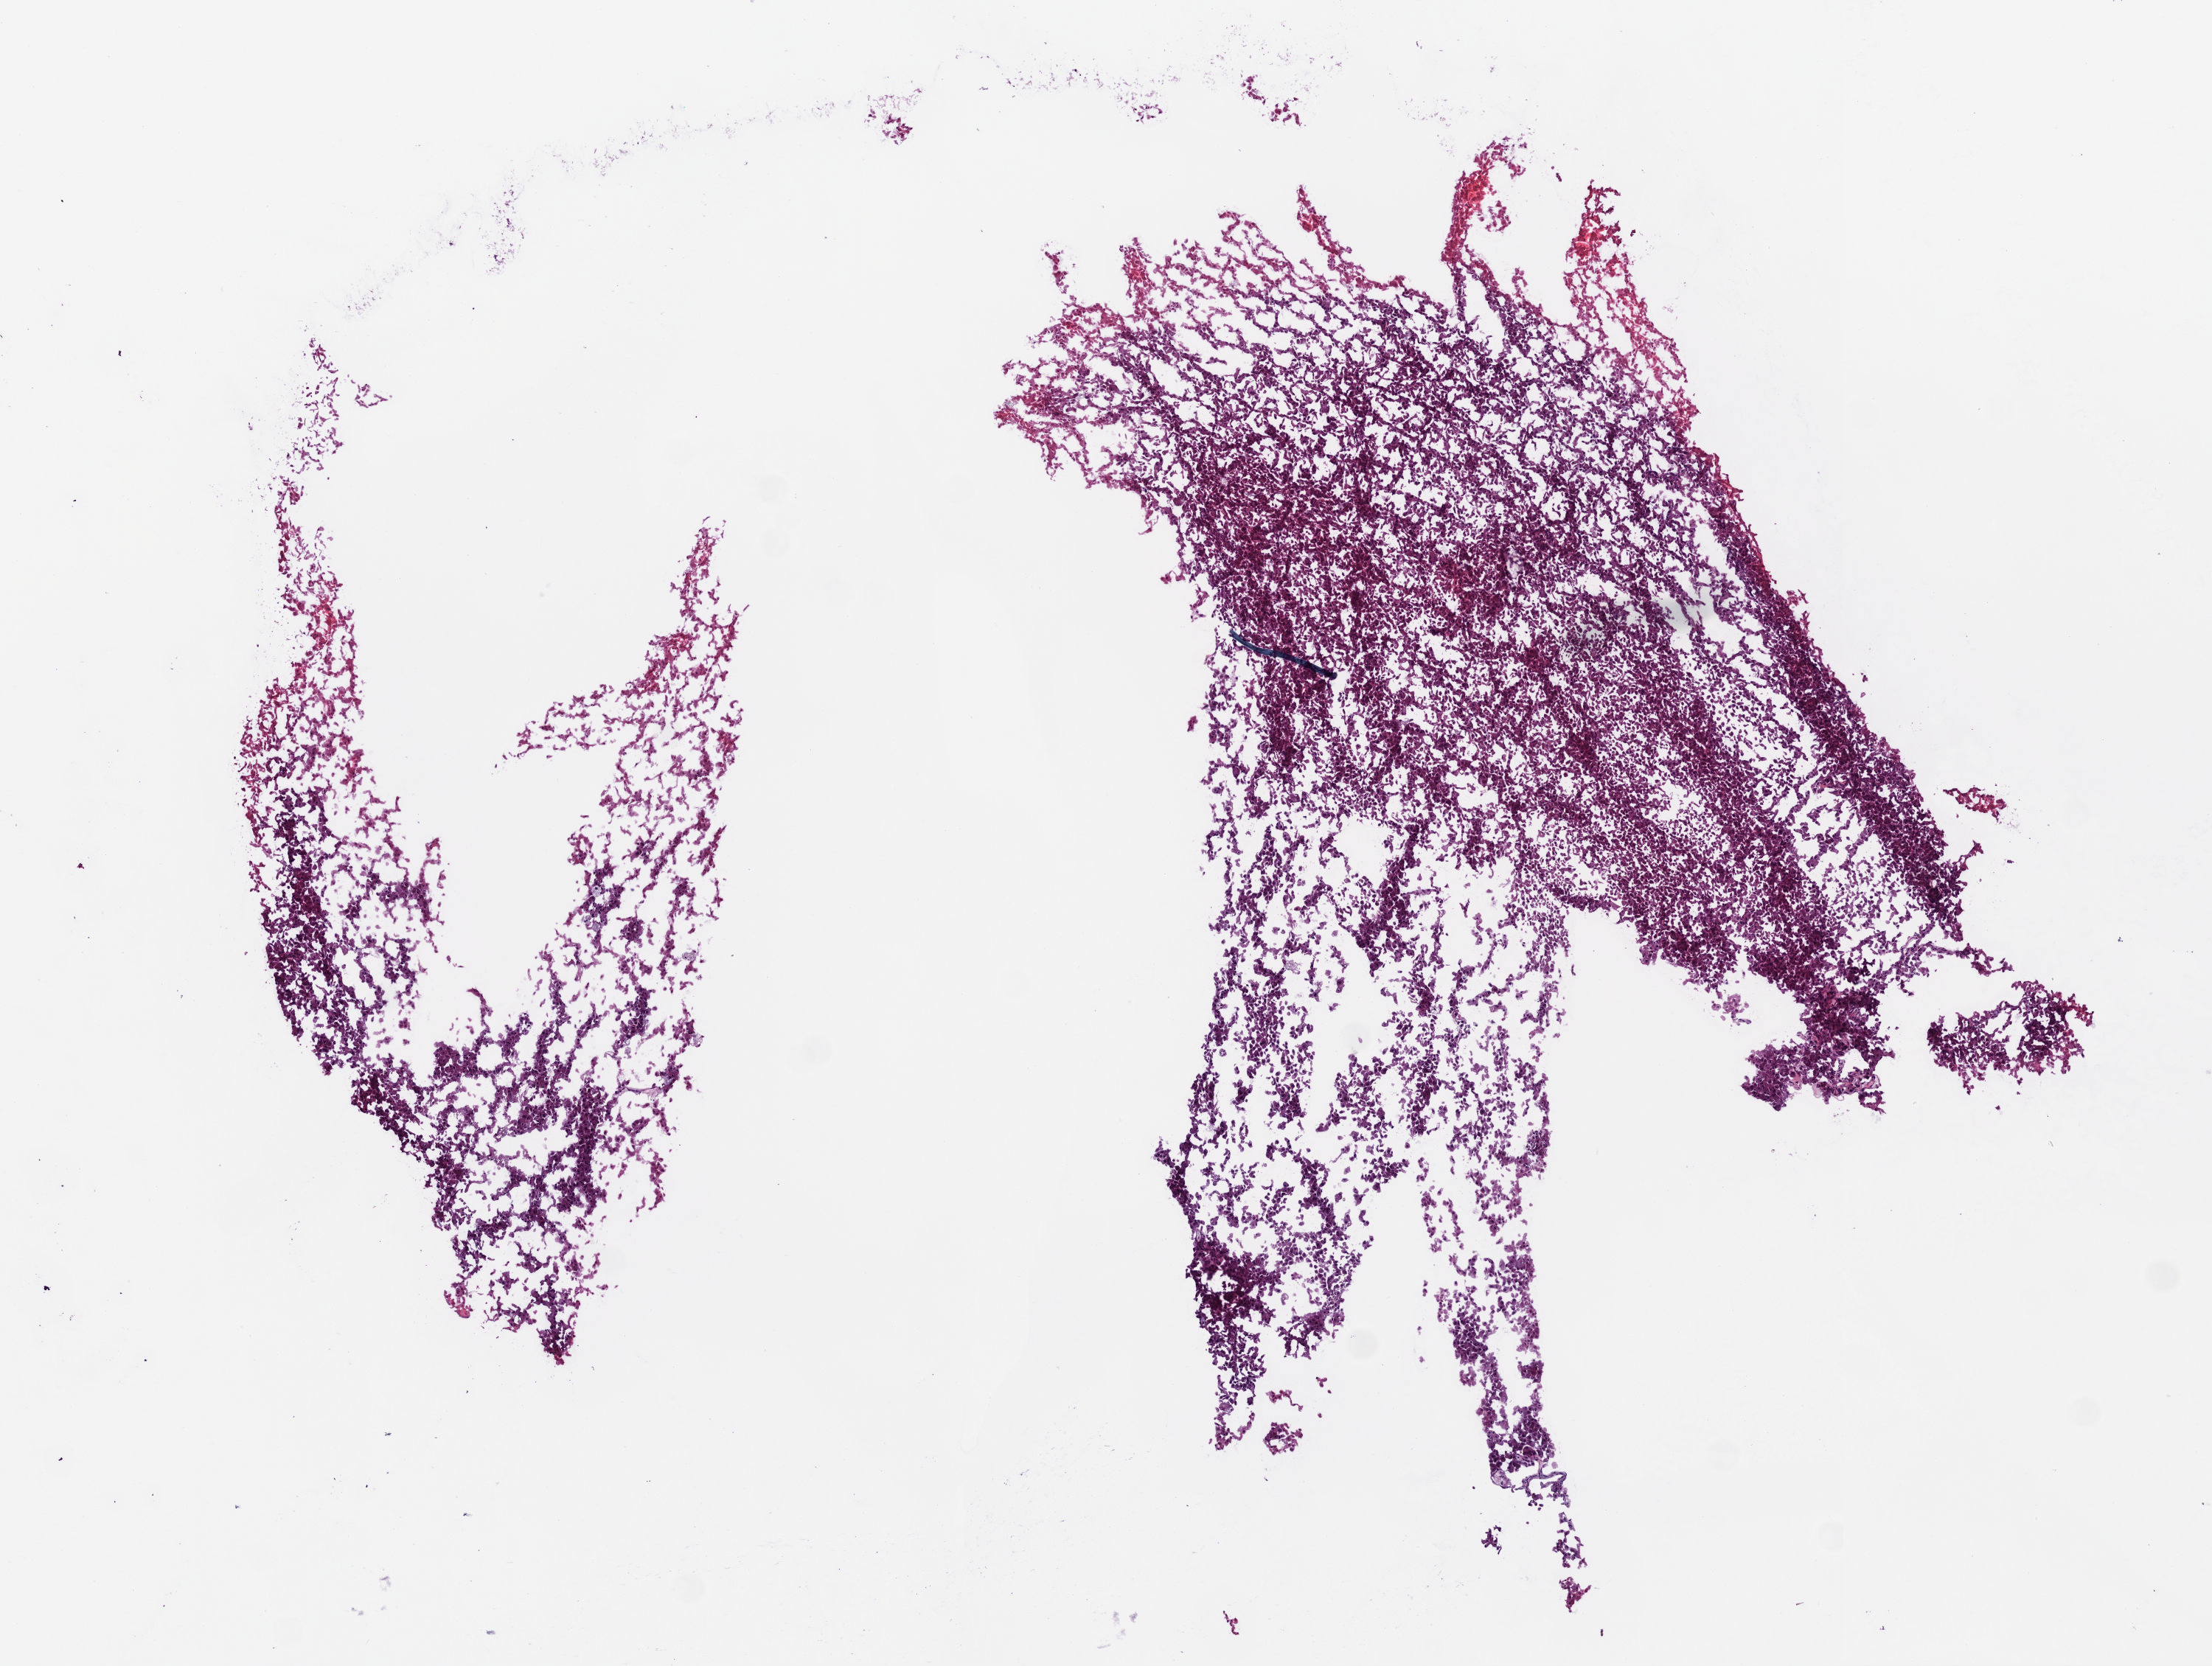
Hematoxylin and eosin (H&E) stained whole-slide image, whole scanned area (about 6.0 x 4.5 mm) shown as a low-resolution overview, frozen section from the bottom of the tissue portion, sample: primary tumour, kidney. Female, age 71 years at initial diagnosis. Histologic grade: GX (grade cannot be assessed). Slide review estimates, as recorded: tumour cells 99%, tumour nuclei 88%, normal cells 1%, stromal cells 0%, necrosis 0%.
TNM: T1b NX M0. Laterality: left. Diagnosis: Clear cell adenocarcinoma, NOS. AJCC pathologic stage: I.